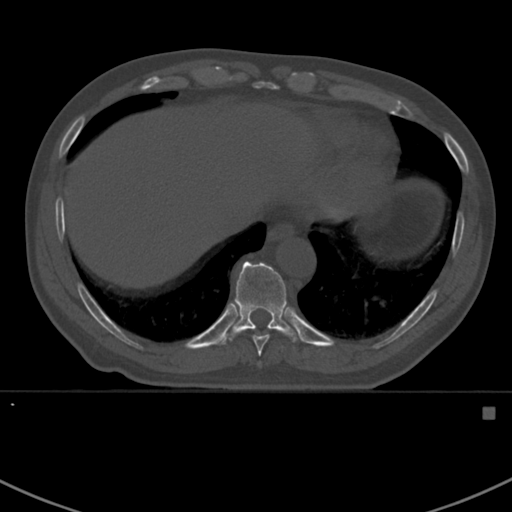
CT including the spine, one axial slice; slice 373 of 412 in the series (ordered by position); reconstruction kernel Br40s; bone window (W 1800 / L 400 HU); 512 × 512 image matrix. Patient: male, 59 years. Case-level facts recorded for this patient, not image findings: primary cancer: prostate.
Outlined on this slice (semi-automatic segmentation, software-assisted and operator-edited):
- T10 vertebra: bounding box [x1, y1, x2, y2] px = [216, 262, 300, 346]
- T9 vertebra: [252, 335, 269, 357]